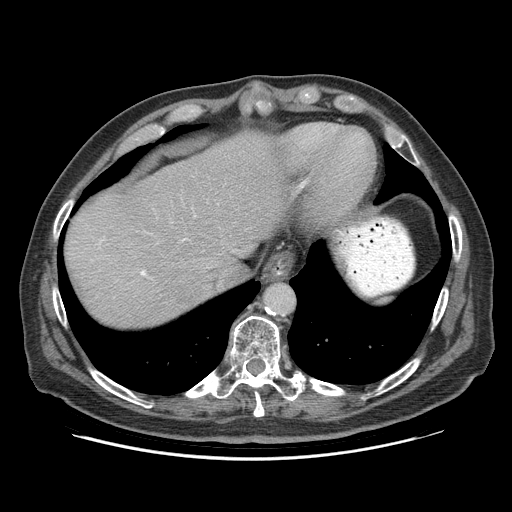
Contrast-enhanced abdominal CT (liver protocol), one axial slice; slice 75 of 95 in the series (ordered by position); reconstruction kernel STANDARD; soft-tissue window (W 400 / L 40 HU); 512 × 512 image matrix. Case-level facts recorded for this patient, not image findings: diagnosis: hepatocellular carcinoma (patient treated with transarterial chemoembolisation; whether this scan precedes or follows treatment is not stated here); TNM stage (as recorded): Stage-IVB; Child-Pugh class: A; tumour differentiation: well differentiated; tumour nodularity: uninodular.
Outlined on this slice (semi-automatically segmented with operator editing):
- abdominal aorta: box from (x=265, y=284) to (x=293, y=313) px
- liver parenchyma outside the tumour (the mass and vessels are separate outlines, so this box may not span the whole liver): (x=66, y=130)–(x=294, y=326)
- liver vessels: (x=141, y=239)–(x=185, y=276)